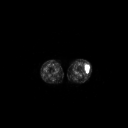
FDG PET of an extremity soft-tissue mass (from a PET/CT study), one axial slice. Position 169 of 223 along the scan axis. 128 × 128 image matrix. Female patient, age 16 years. Case-level facts recorded for this patient, not image findings: histological type: spindle cell suggestive of biphasic synovial sarcoma; grade: intermediate; site of the primary tumour: left knee.
Structures marked on this image (expert contour drawn on MRI and transferred to this co-registered scan by the dataset authors):
- gross tumour volume including surrounding oedema: bounding box [x1, y1, x2, y2] px = [85, 65, 89, 73]
- gross tumour volume (mass): [85, 65, 89, 73]